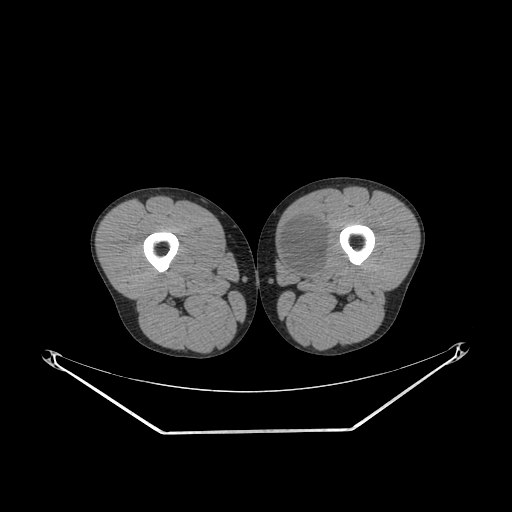
CT of an extremity soft-tissue mass (from a PET/CT study), one axial slice. Slice 243 of 311 in the series (ordered by position). Reconstruction kernel SOFT. 140 kVp. Soft-tissue window (W 400 / L 40 HU). 3.75 mm slice thickness. 512 × 512 image matrix, field of view 500 × 500 mm. Male patient. Case-level facts recorded for this patient, not image findings: histological type: mixoid liposarcoma; grade: low; site of the primary tumour: left thigh.
Outlined on this slice (expert contour drawn on MRI and transferred to this co-registered scan by the dataset authors):
- gross tumour volume (mass): bounding box <279,215,328,275> (left, top, right, bottom; pixels)